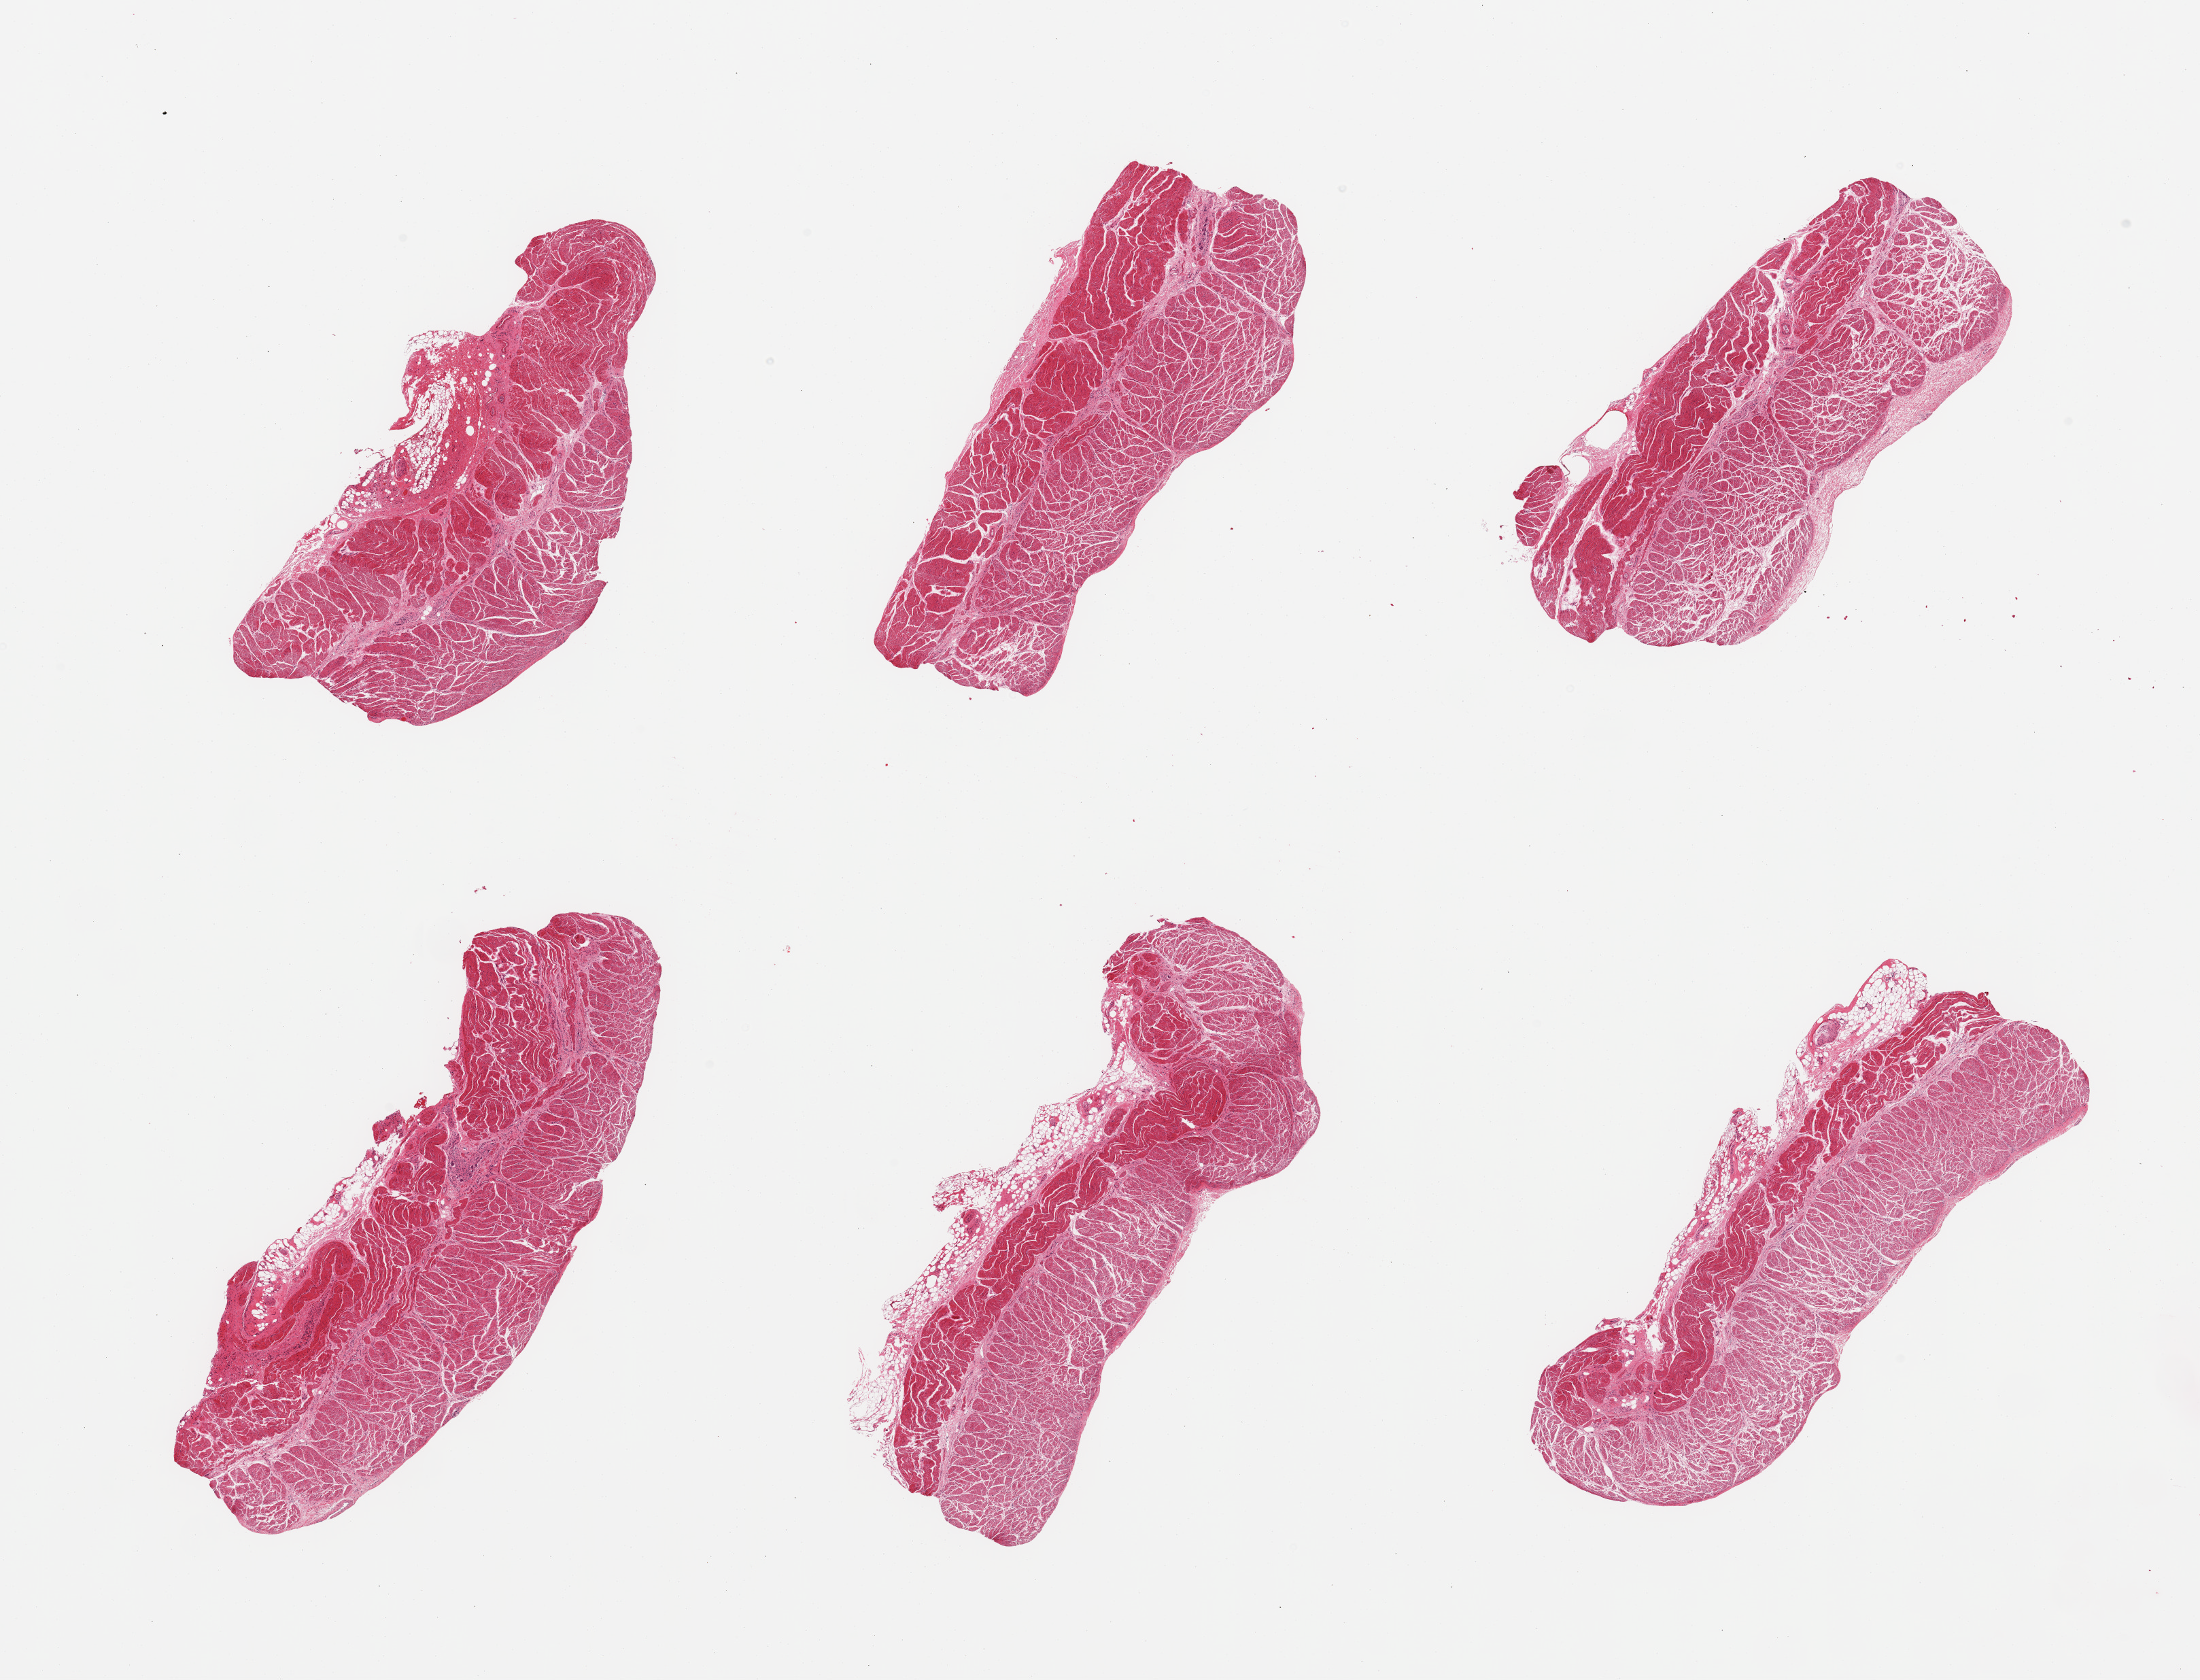
Whole-slide image, haematoxylin and eosin stain, a low-resolution overview of the entire scanned area, about 25.6 x 19.5 mm; PAXgene-fixed paraffin-embedded (PFPE) section; section of esophageal muscle (target tissue); tissue donor sample. Donor: male.
Review note (as recorded): 6 pieces. confirmed target muscularis.